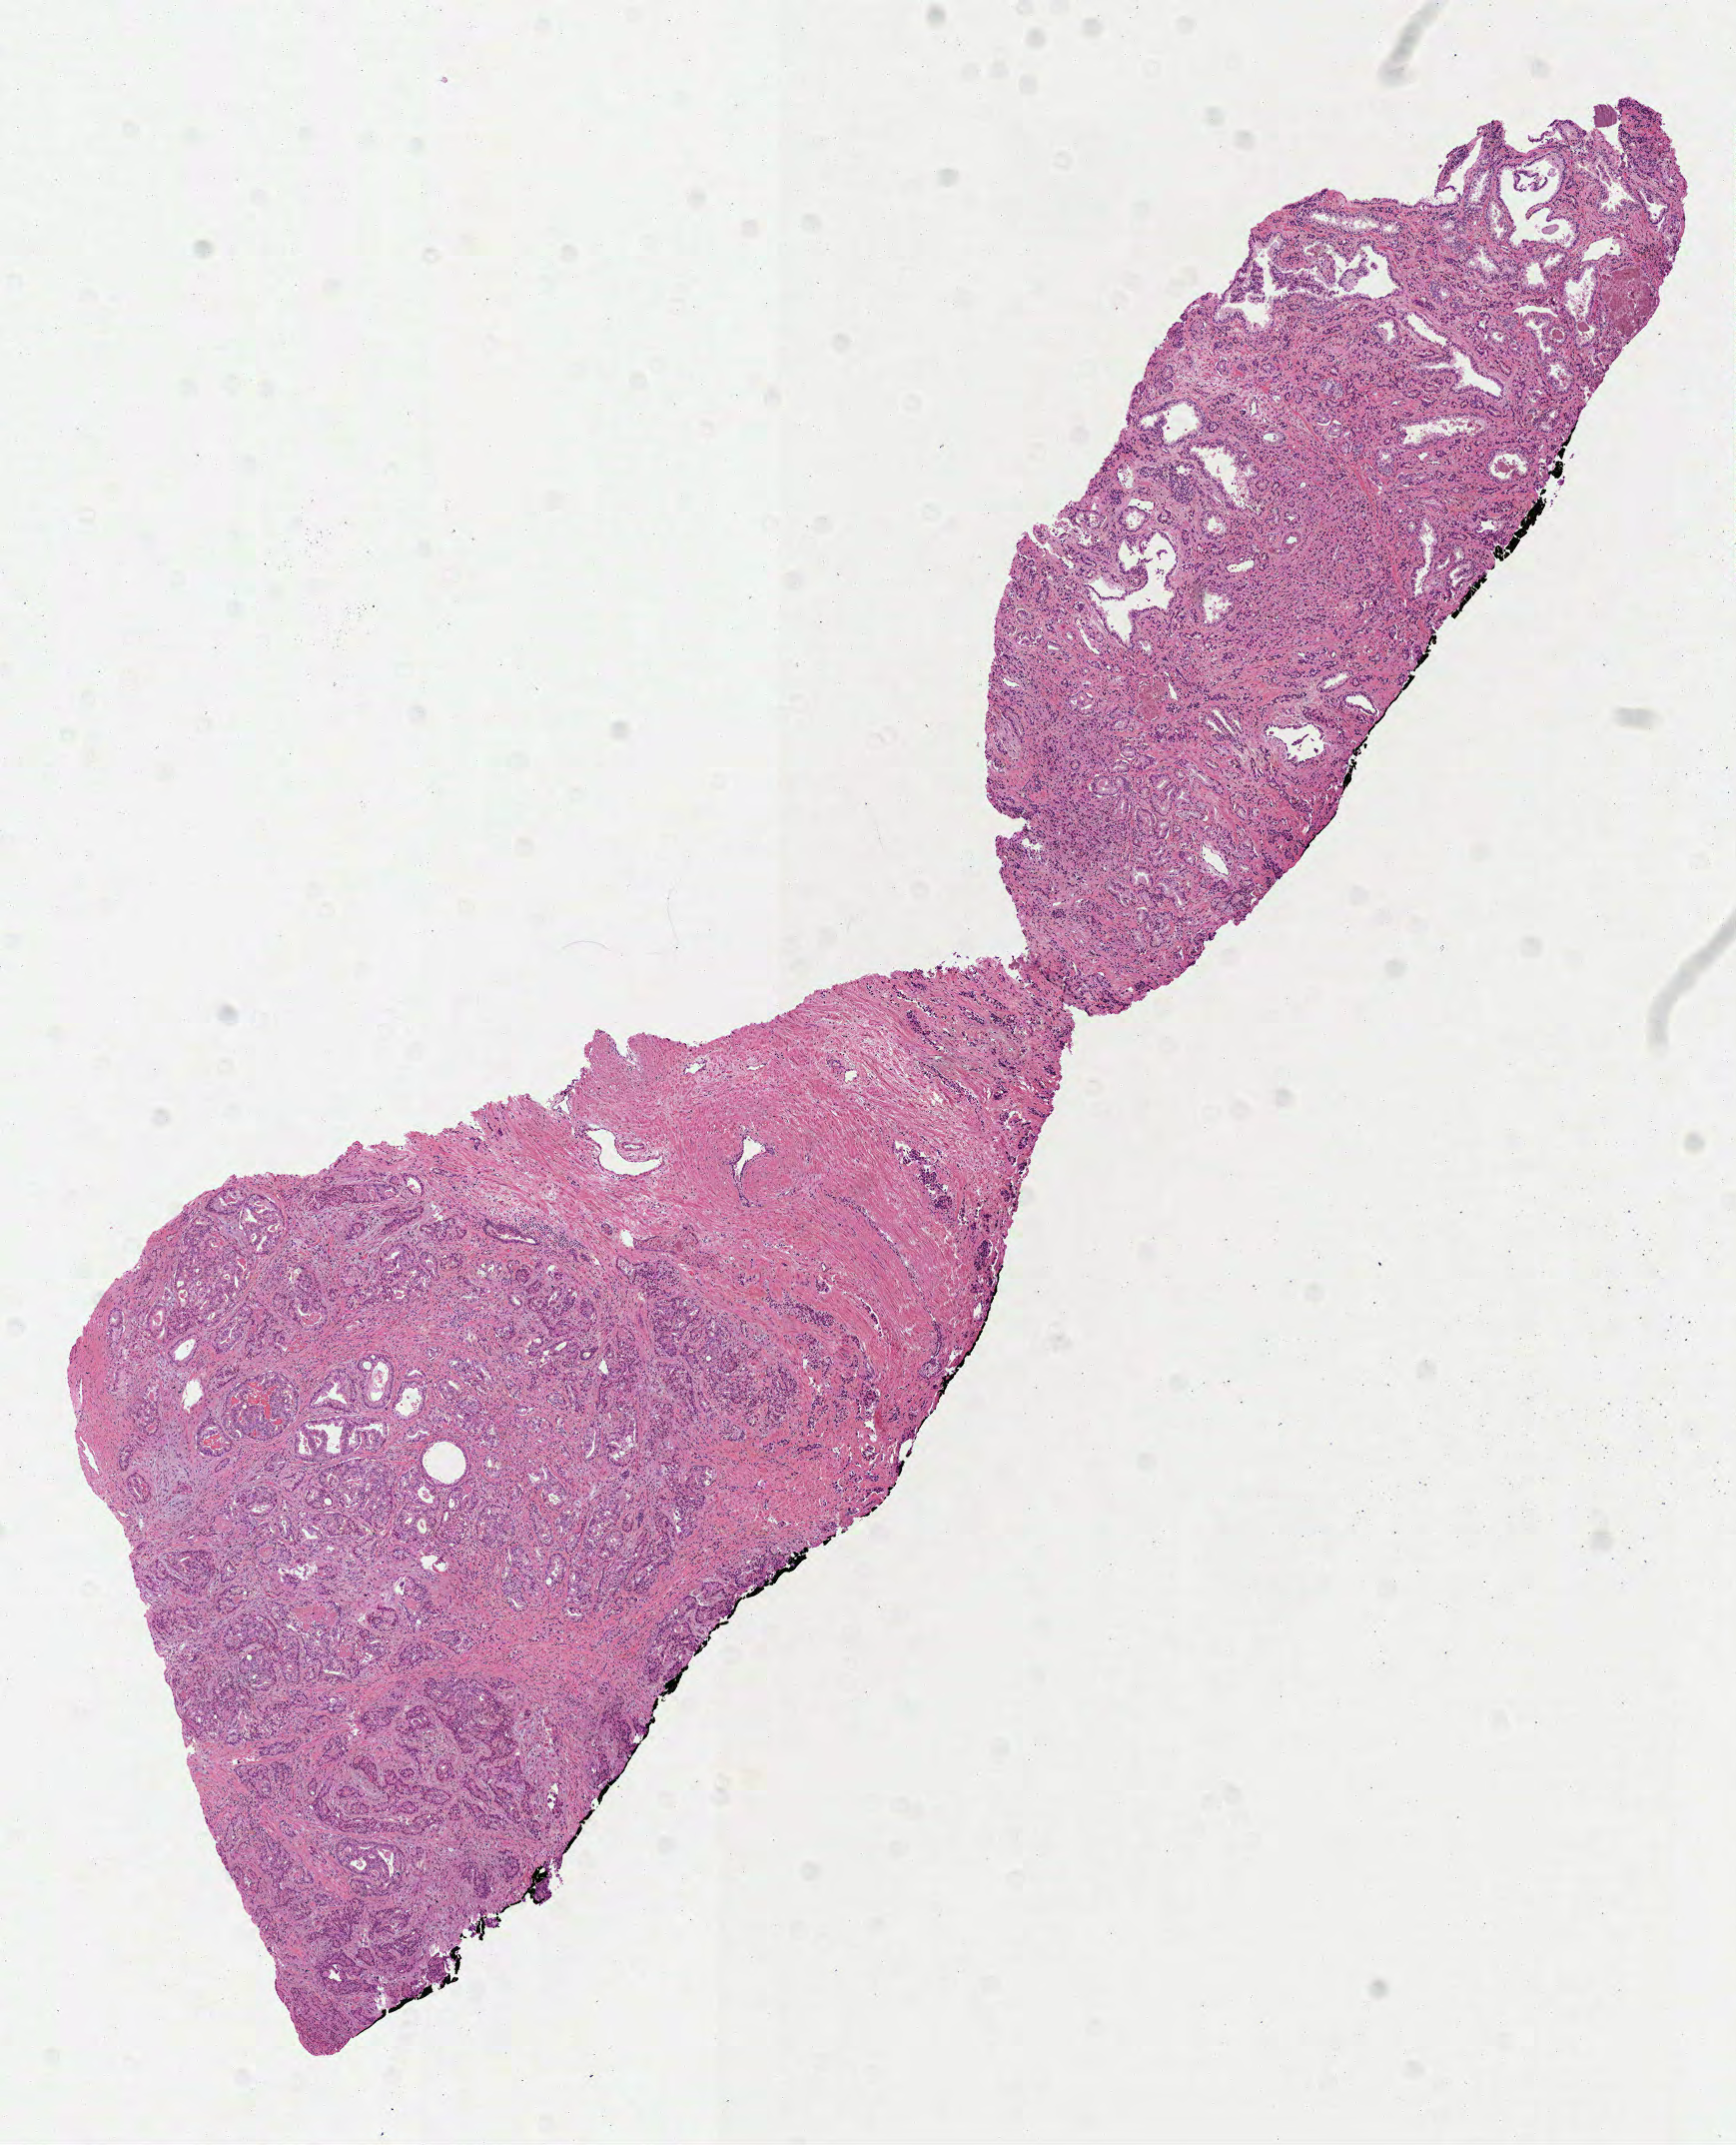
Whole-slide histology image, H&E-stained — a low-resolution overview of the entire scanned area, about 7.0 x 8.7 mm (acquisition: 40x scan). FFPE section. Primary tumour sample from the prostate. Male, age 70 years at initial diagnosis. Gleason score: 7 (3+4).
* lymph nodes positive (case pathology): 1 of 8 examined
* pathologic diagnosis: Acinar cell carcinoma (prostate gland)
* laterality: bilateral